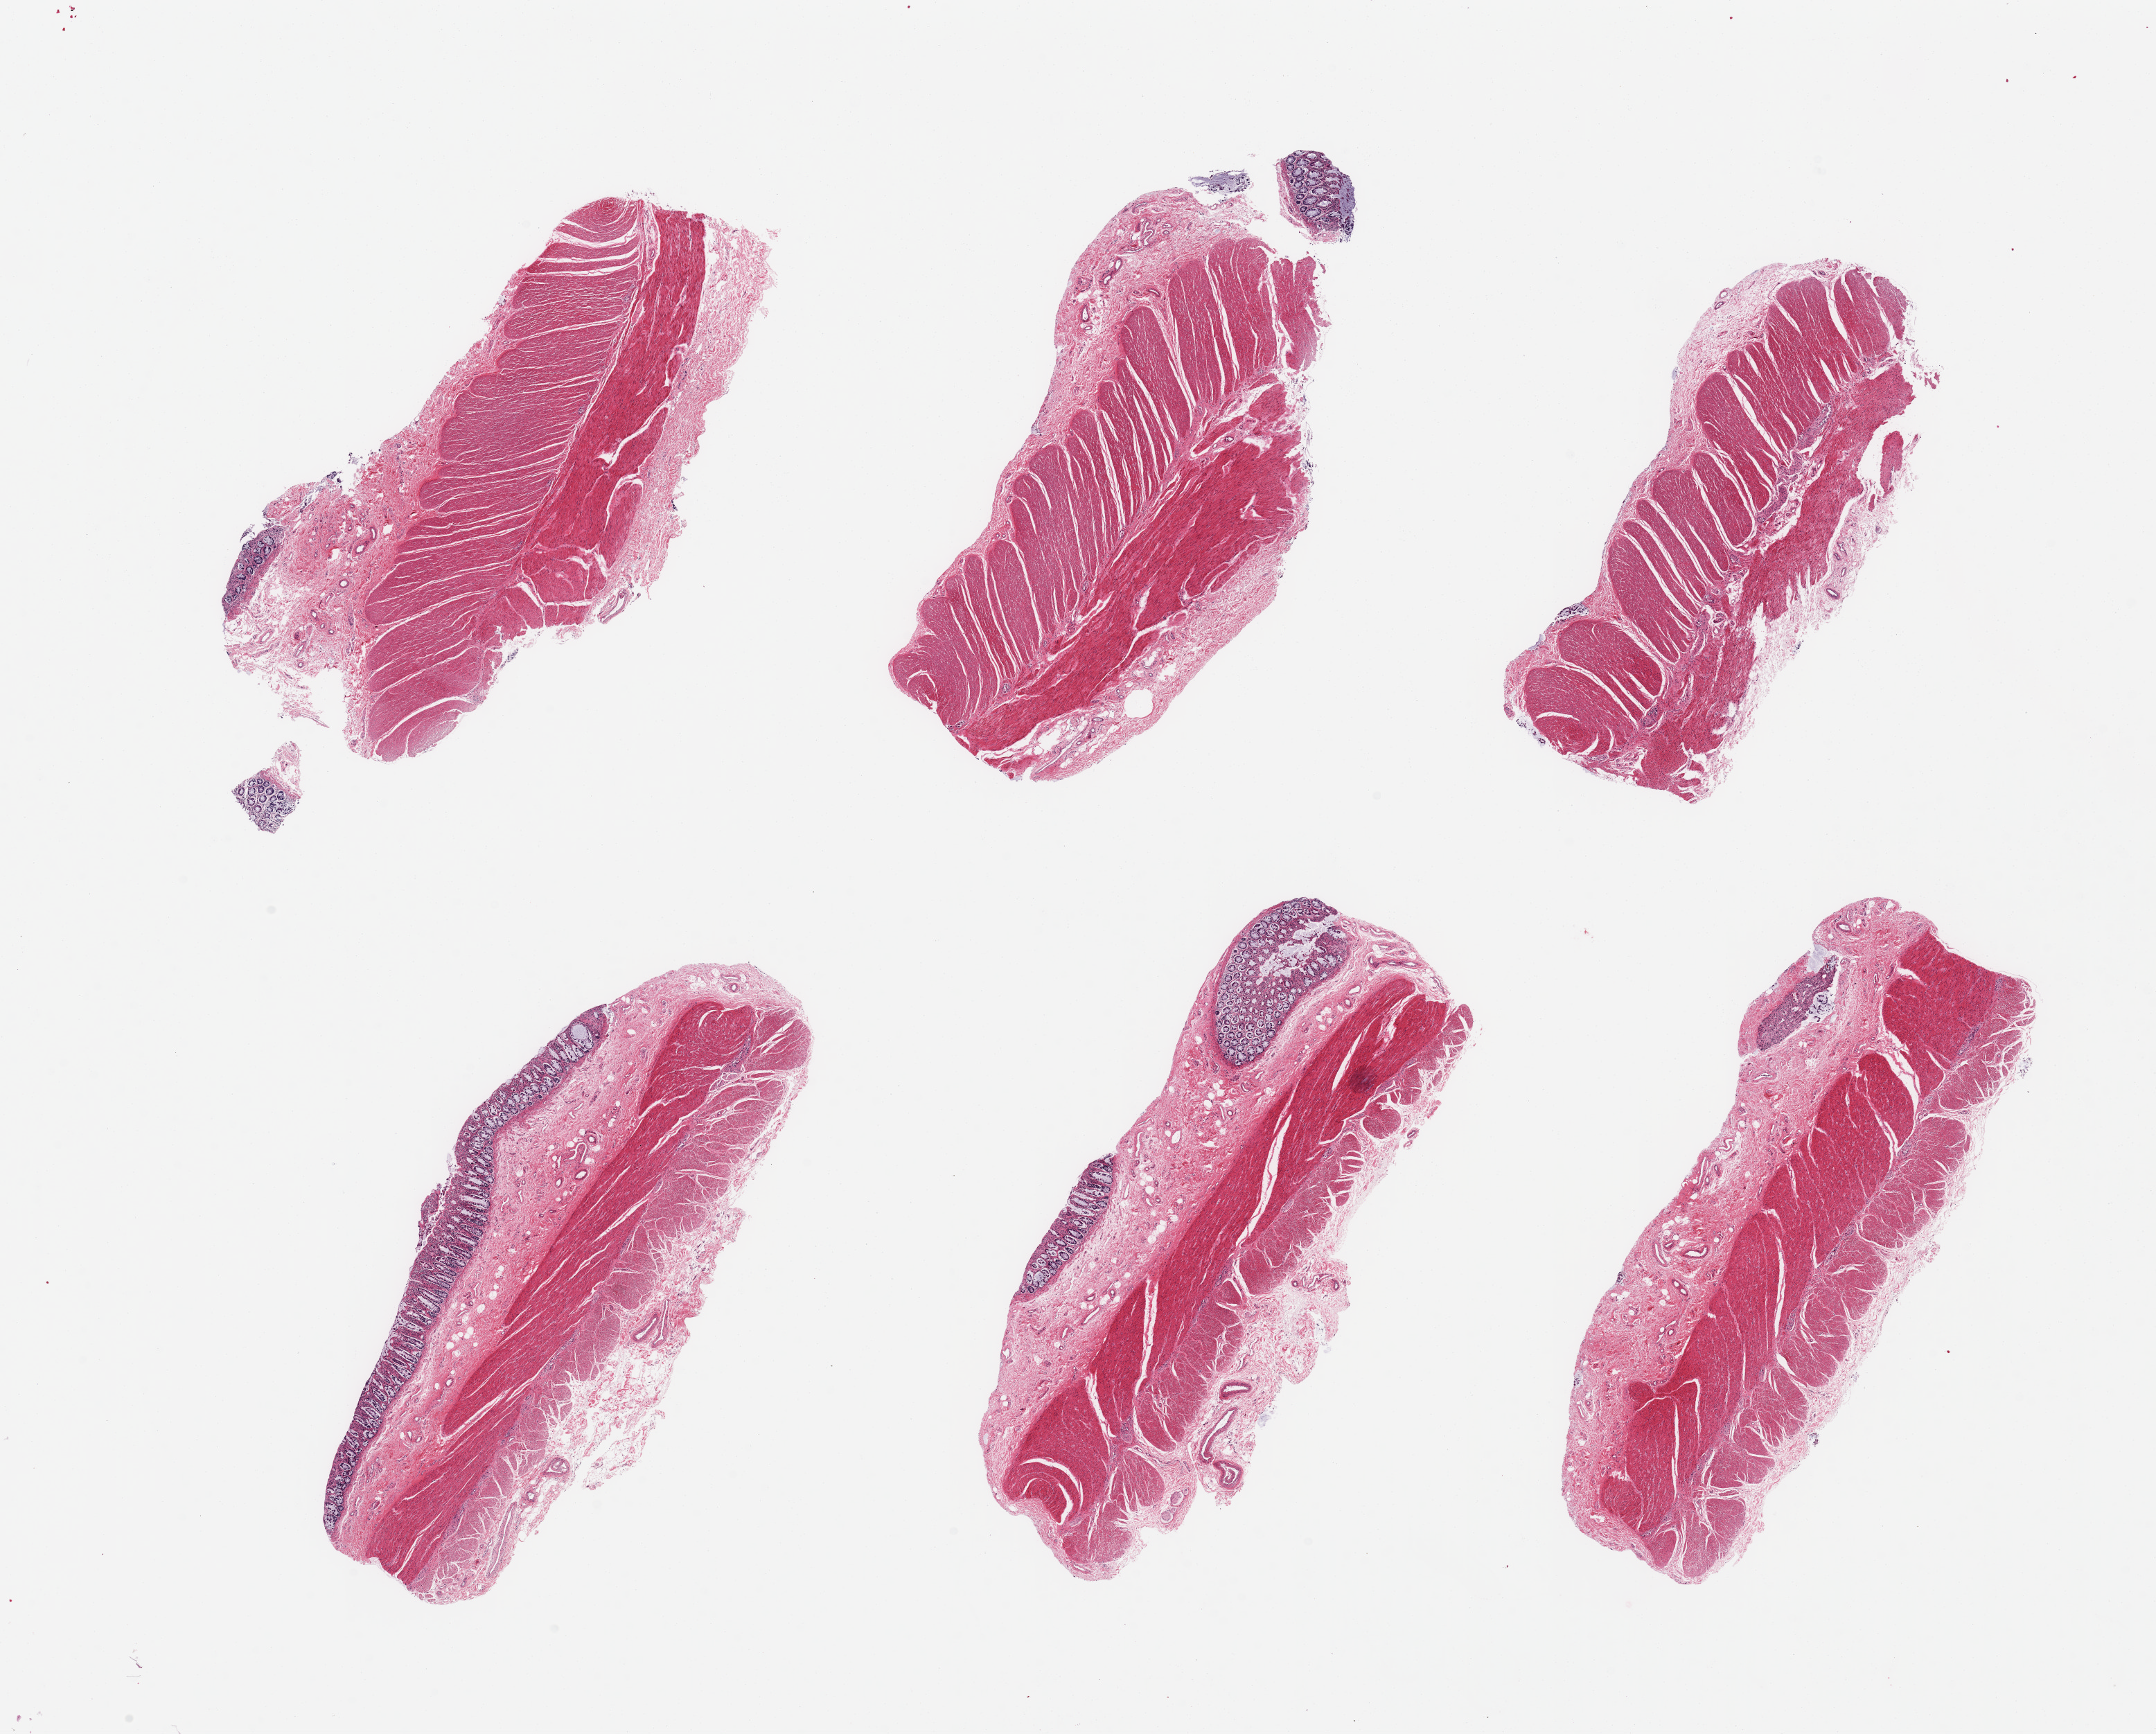
Whole-slide image, haematoxylin and eosin stain, brightfield — whole scanned area (about 24.6 x 19.8 mm, slide scanned at 20x) shown as a low-resolution overview. Male donor.
Specimen: PAXgene-fixed paraffin-embedded (PFPE) section; sampled site (target tissue): sigmoid colon; tissue donor sample.